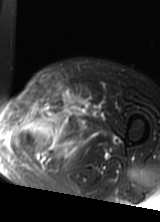
MRI of an extremity soft-tissue mass, one axial slice; position 46 of 69 along the scan axis; T2-weighted fat-saturated; MR volume resampled by the dataset authors to the PET/CT grid (not the native acquisition matrix); 3.27 mm slice thickness; 160 × 222 image matrix. Female patient. Case-level facts recorded for this patient, not image findings: histological type: pleomorphic leiomyosarcoma; grade: high; site of the primary tumour: left thigh.
Structures marked on this image (expert contour drawn on MRI and transferred to this co-registered scan by the dataset authors):
- gross tumour volume including surrounding oedema: bounding box [x1, y1, x2, y2] px = [16, 91, 90, 162]